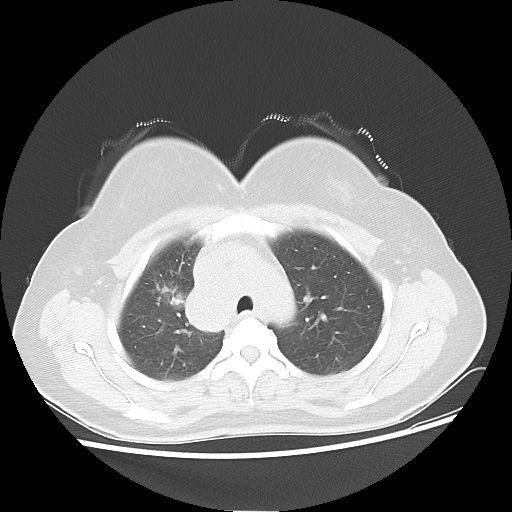
Chest CT, one axial slice. Slice 38 of 50 in the series (ordered by position). Reconstruction kernel LUNG. 100 kVp. Lung window (W 1500 / L -600 HU). 512 × 512 image matrix. Patient: female, 40 years. From the clinical record (not read from this slice): clinical TNM (as recorded): T1c N3 M0.
Structures marked on this image (bounding box drawn by a radiologist):
- lung tumour (recorded histology: small cell carcinoma): bounding box [x1, y1, x2, y2] px = [151, 279, 184, 323]